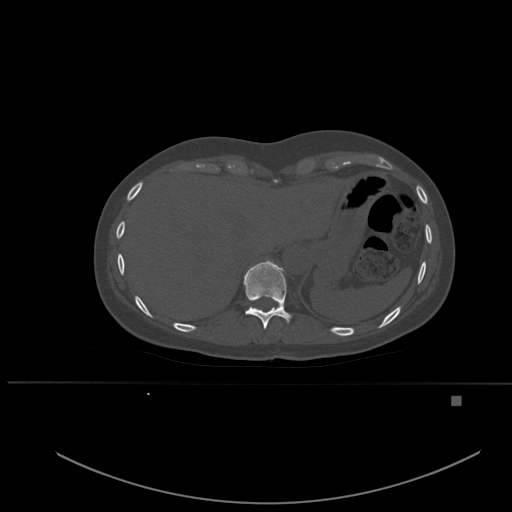
CT including the spine, one axial slice; position 288 of 651 along the scan axis; bone window (W 1800 / L 400 HU); 512 × 512 image matrix, field of view 443 × 443 mm. Patient: female, 49 years. Case-level facts recorded for this patient, not image findings: primary cancer: breast; vertebrae with lytic lesions (as recorded): L3, T12, L4.
Structures marked on this image (semi-automatic segmentation, software-assisted and operator-edited):
- T10 vertebra: bounding box <243,260,292,329> (left, top, right, bottom; pixels)